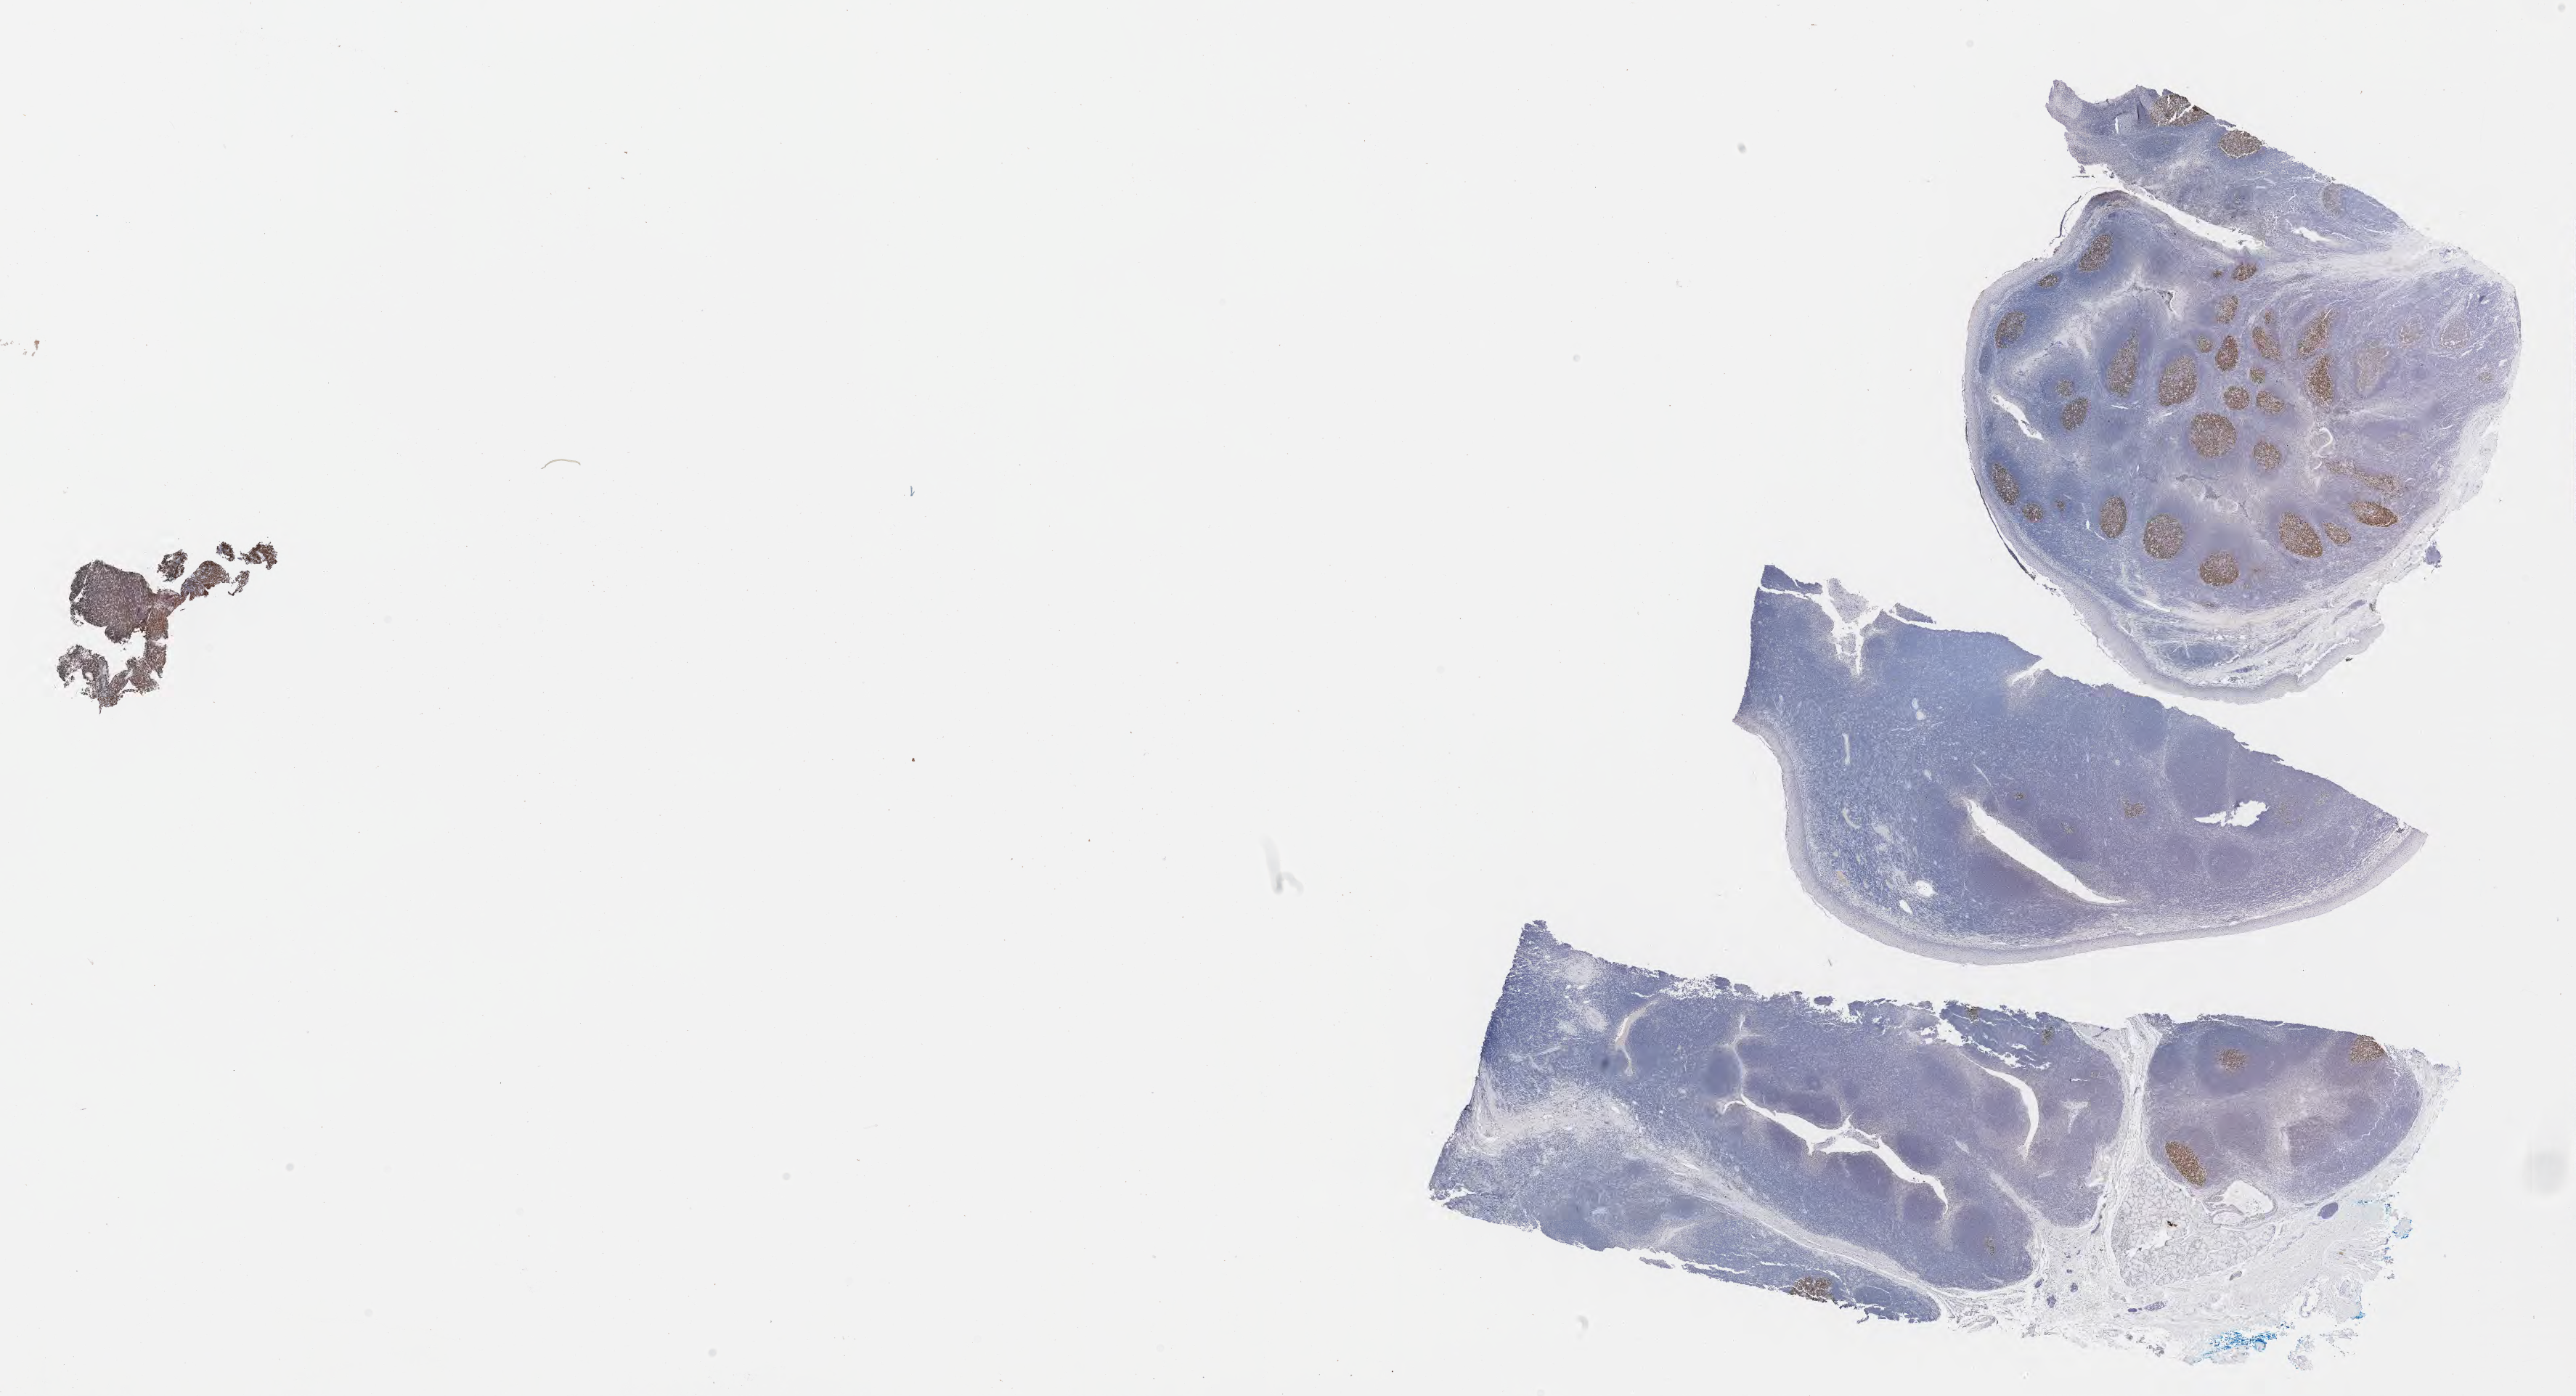
Whole-slide image, immunohistochemical stain for BCL6, a low-resolution overview of the entire scanned area, about 28.7 x 15.5 mm. Specimen: tumor tissue. Patient: male, age at initial diagnosis 8 years.
• diagnosis: Burkitt lymphoma, NOS